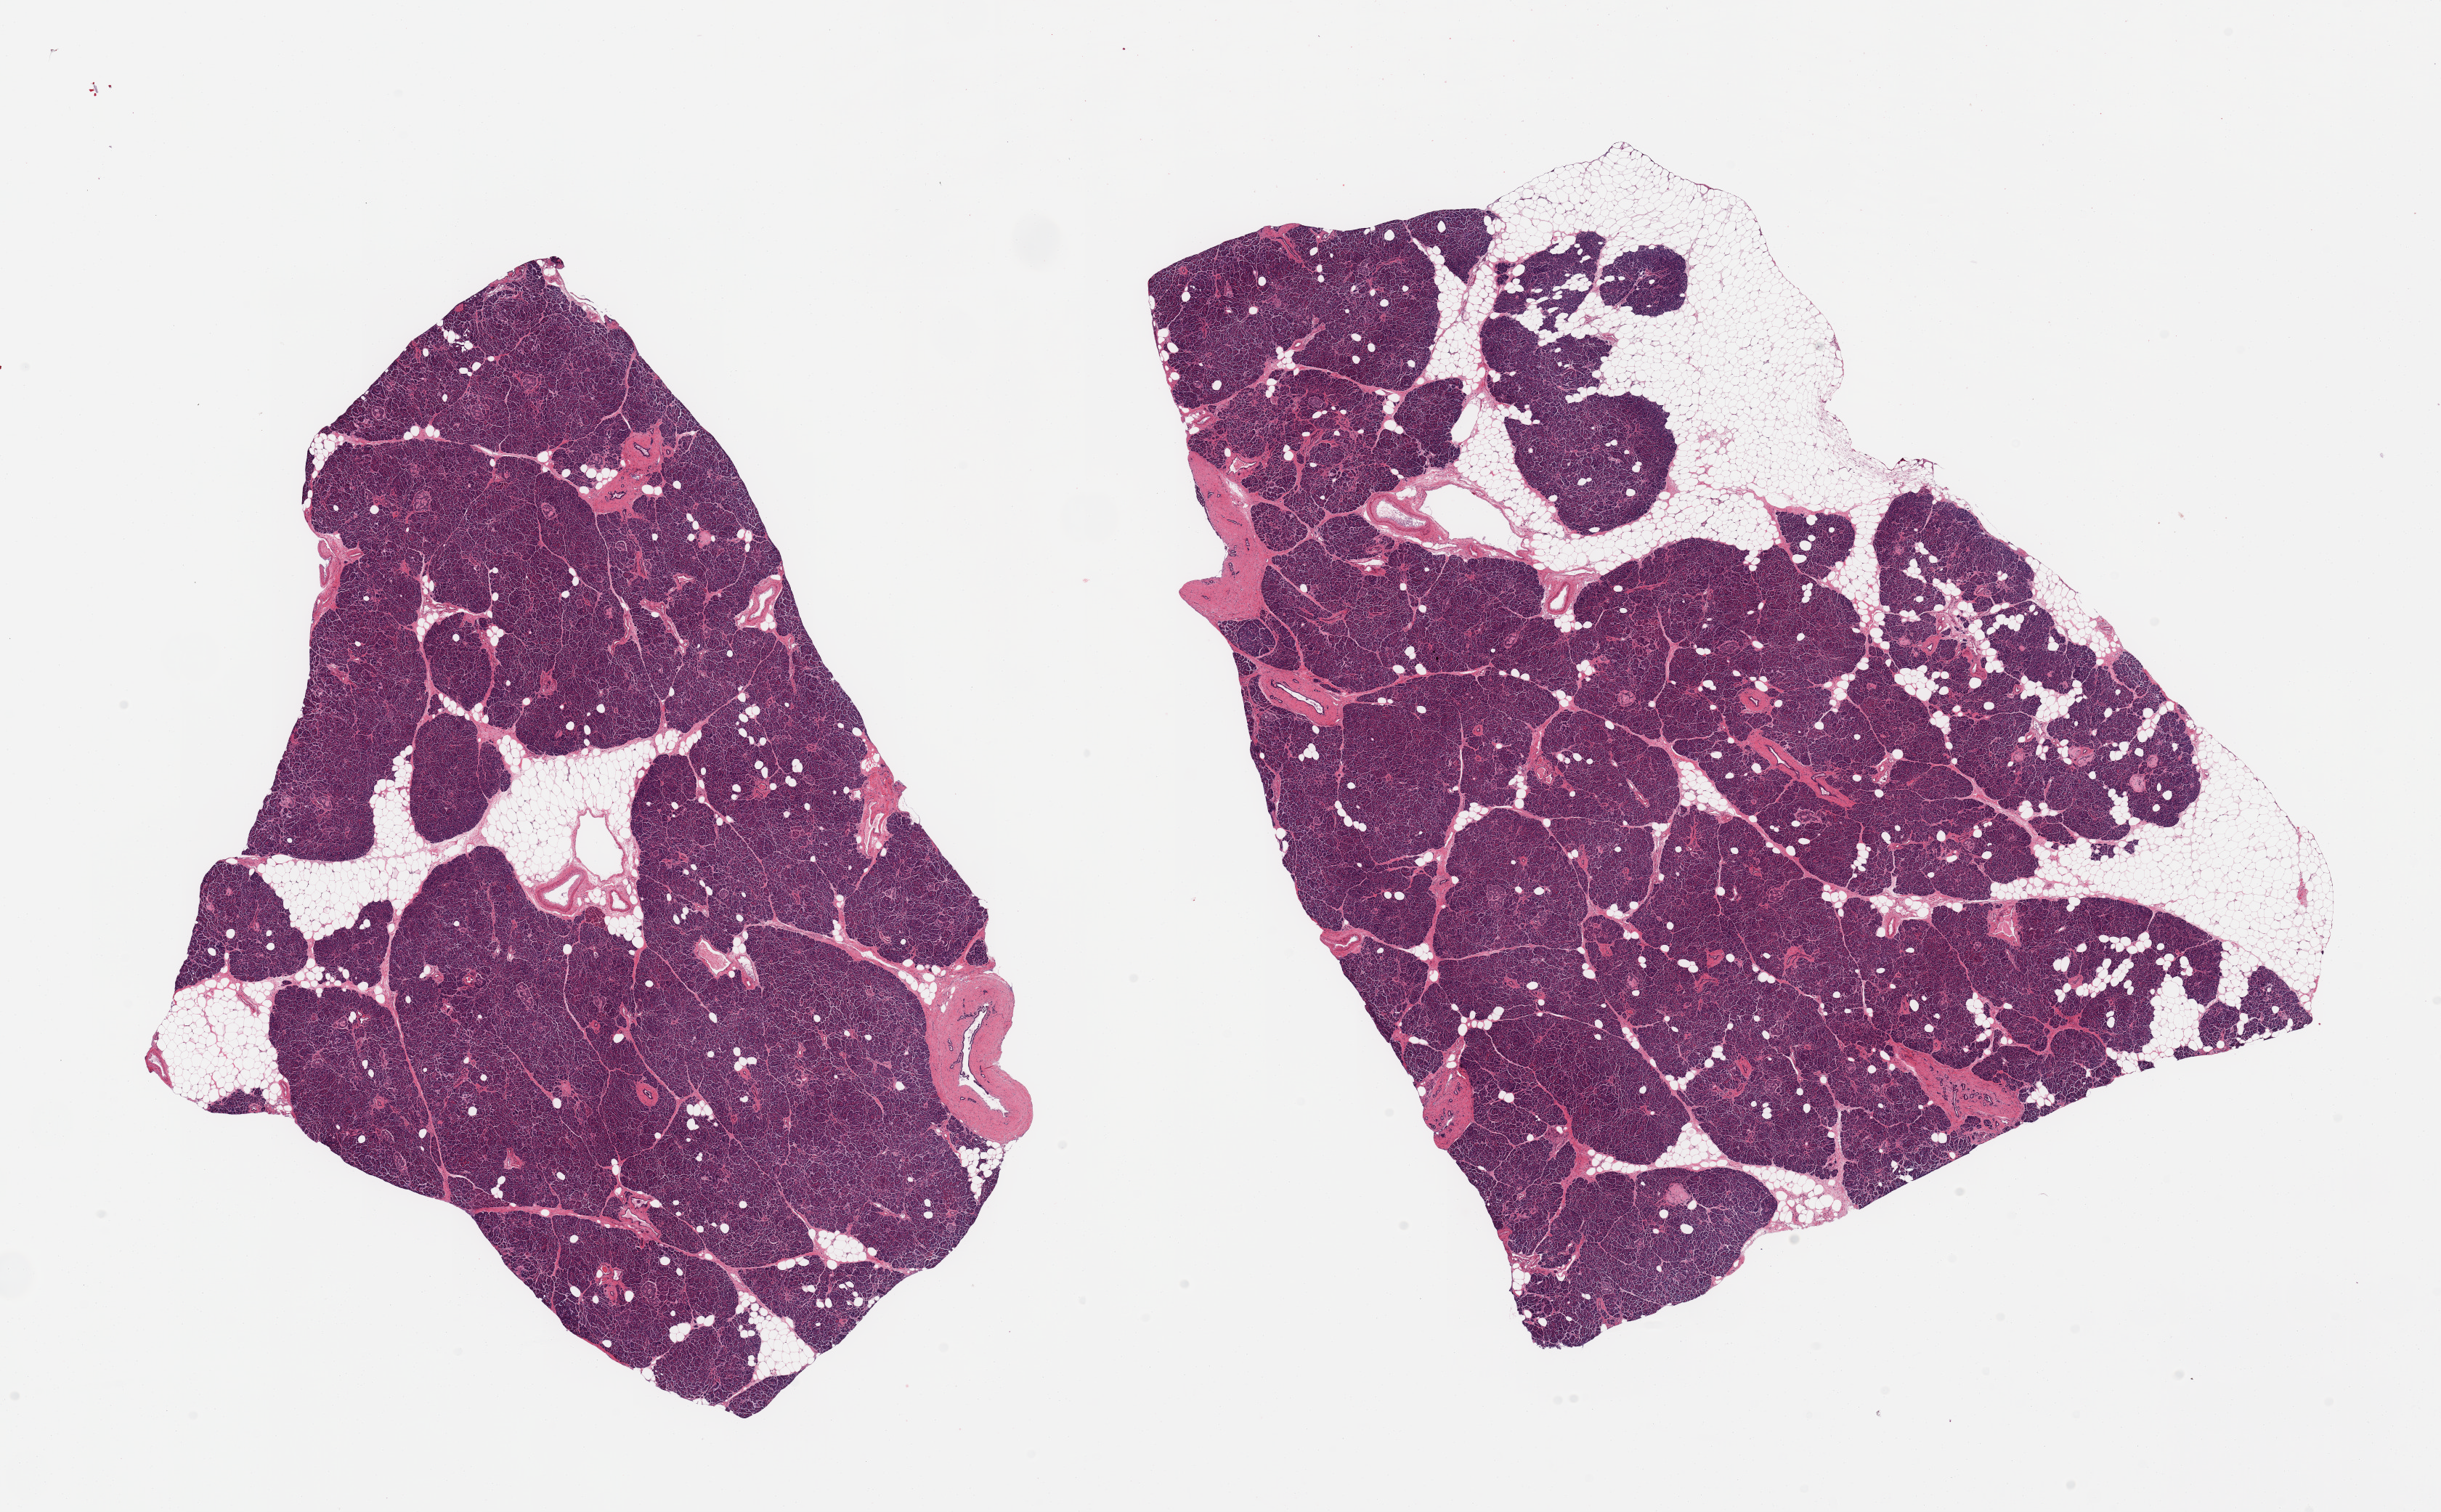
Digitized hematoxylin and eosin (H&E)-stained section, brightfield, a low-resolution overview of the entire scanned area, about 26.6 x 16.5 mm. PAXgene-fixed, paraffin-embedded tissue. Section of pancreas (target tissue). Tissue donor sample. Male donor.
Pathologist's review note for this sample: 2 pieces, islets rare but well -preserved; ~15% adherent fat.